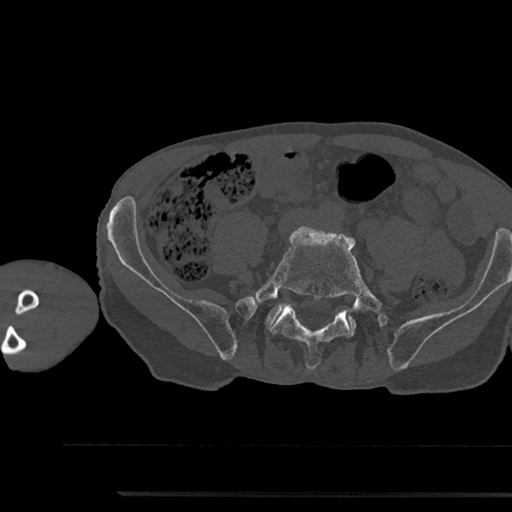
CT including the spine, one axial slice. Position 342 of 797 along the scan axis. Bone window (W 1800 / L 400 HU). 0.5 mm slice thickness. 512 × 512 image matrix, field of view 367 × 367 mm. Male patient, age 79 years. From the clinical record (not read from this slice): primary cancer: prostate.
Outlined on this slice (semi-automatically segmented with operator editing):
- L5 vertebra: bounding box [x1, y1, x2, y2] px = [253, 226, 382, 370]